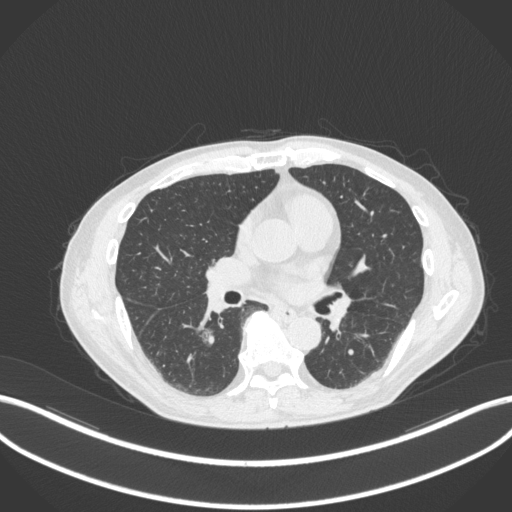
Chest CT, one axial slice; slice 164 of 324 in the series (ordered by position); reconstruction kernel B31f; lung window (W 1500 / L -600 HU); 1 mm slice thickness; 512 × 512 image matrix, field of view 400 × 400 mm. Male patient, age 61 years. Case-level facts recorded for this patient, not image findings: clinical TNM (as recorded): T1c N0 M0.
Annotated regions visible in this slice (bounding box drawn by a radiologist):
- lung tumour (recorded histology: adenocarcinoma): box from (x=197, y=325) to (x=219, y=350) px